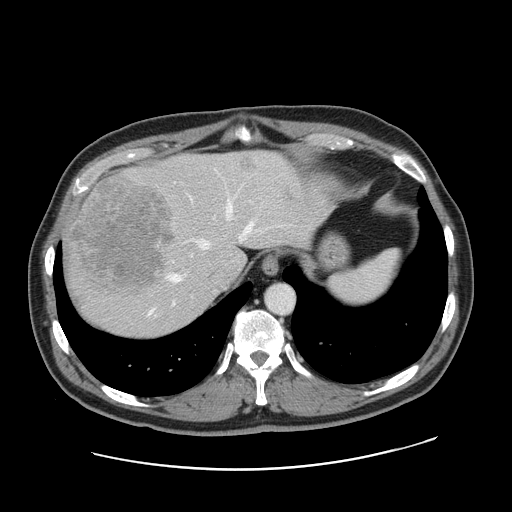
Contrast-enhanced abdominal CT, one axial slice. Position 131 of 178 along the scan axis. Intravenous contrast given. Soft-tissue window (W 400 / L 40 HU). 2.5 mm slice thickness. 512 × 512 image matrix, field of view 403 × 403 mm. Male patient, age 63 years. From the clinical record (not read from this slice): diagnosis: colorectal cancer liver metastases, imaged before liver resection.
Structures marked on this image (expert manual segmentation):
- hepatic veins: bounding box <149,202,252,314> (left, top, right, bottom; pixels)
- liver: <64,151,313,338>
- planned liver remnant (the part of the liver to remain after resection): <157,153,313,279>
- liver metastasis: <243,157,254,170>
- liver metastasis: <70,179,174,290>